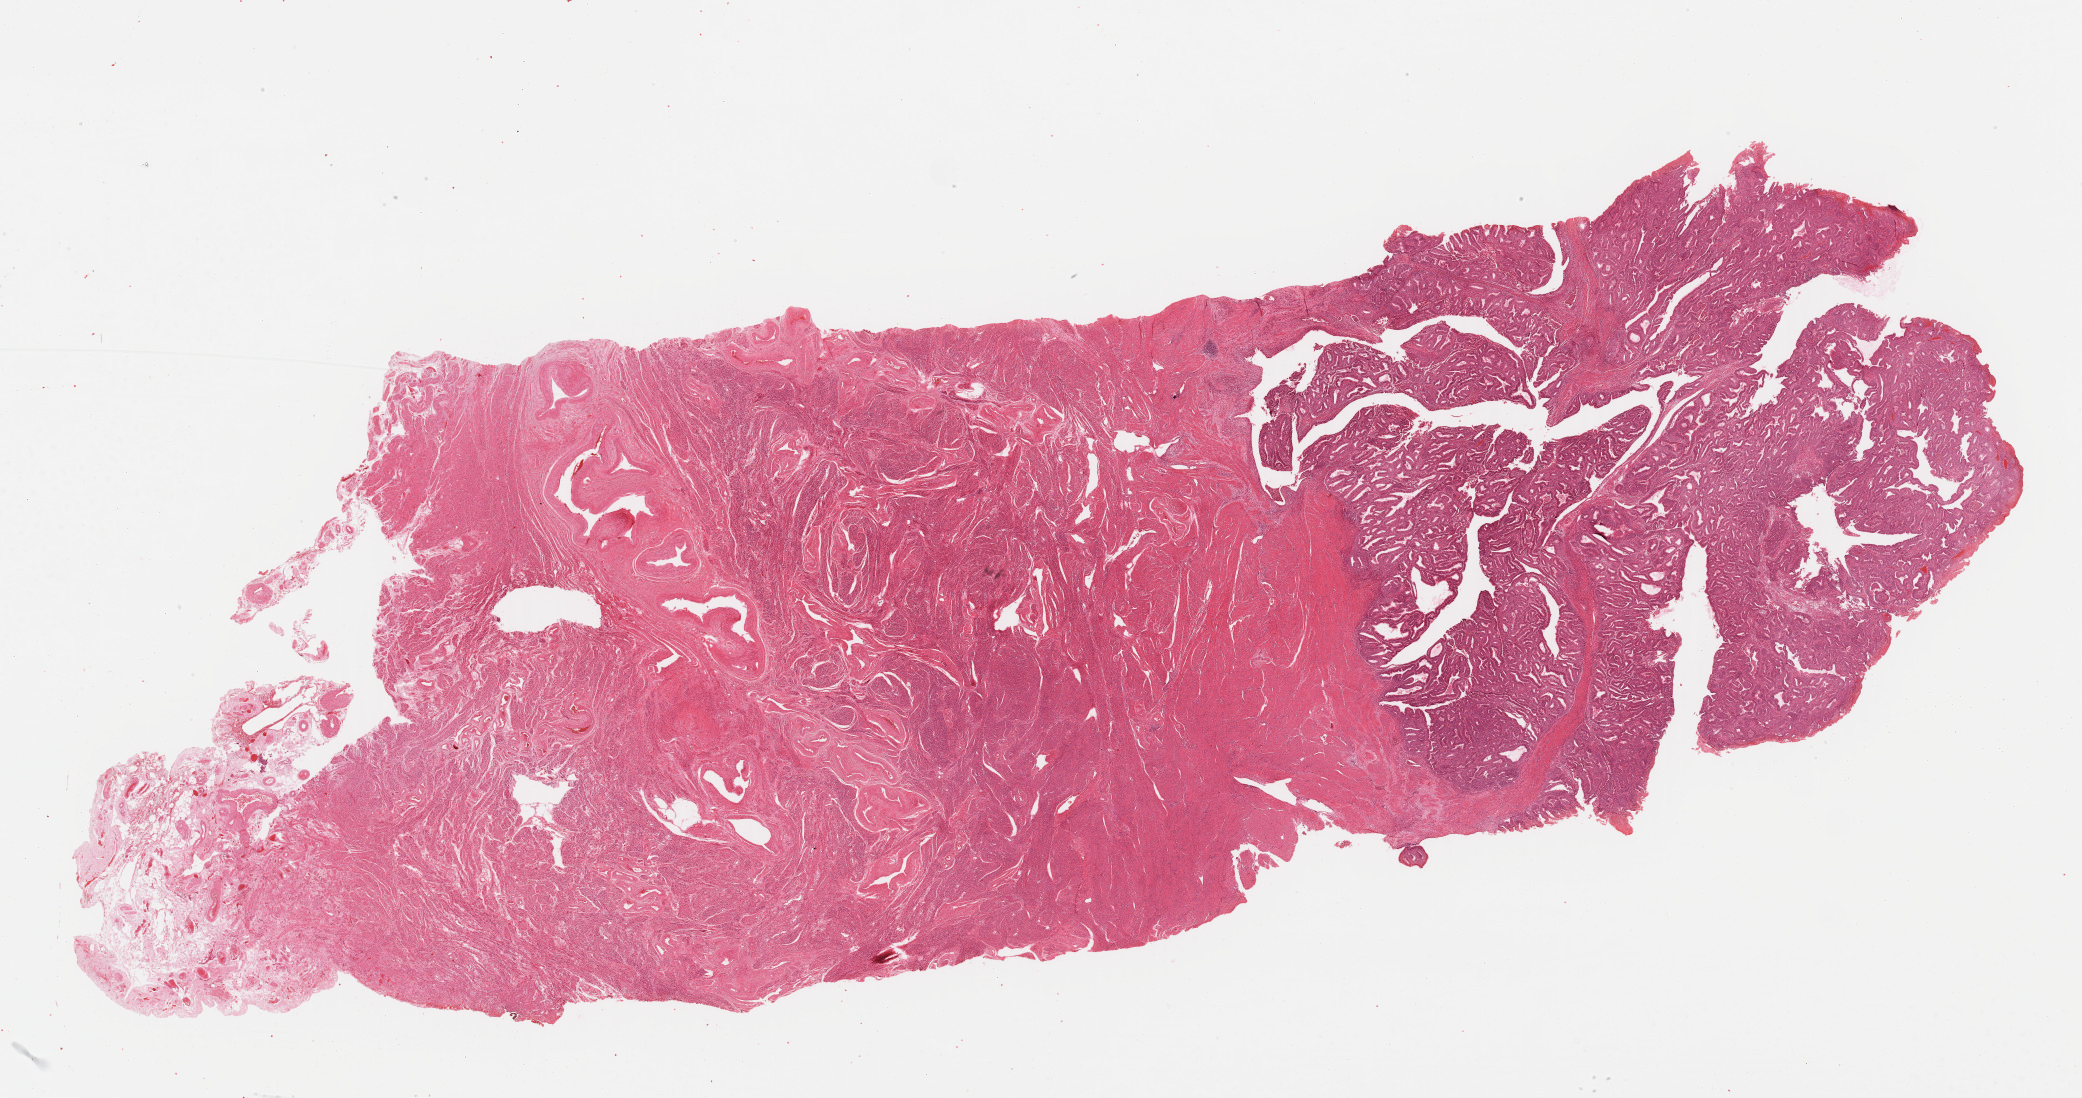
Hematoxylin and eosin (H&E) stained whole-slide image — low-resolution overview of the scanned area, about 32.9 x 17.3 mm (slide scanned at 40x), formalin-fixed paraffin-embedded (FFPE) diagnostic section, uterus, primary tumour sample. Patient: female, age at initial diagnosis 63 years. Histologic grade: G1 (well differentiated).
FIGO stage: IB. Histologic diagnosis: Endometrioid adenocarcinoma, NOS (endometrium).